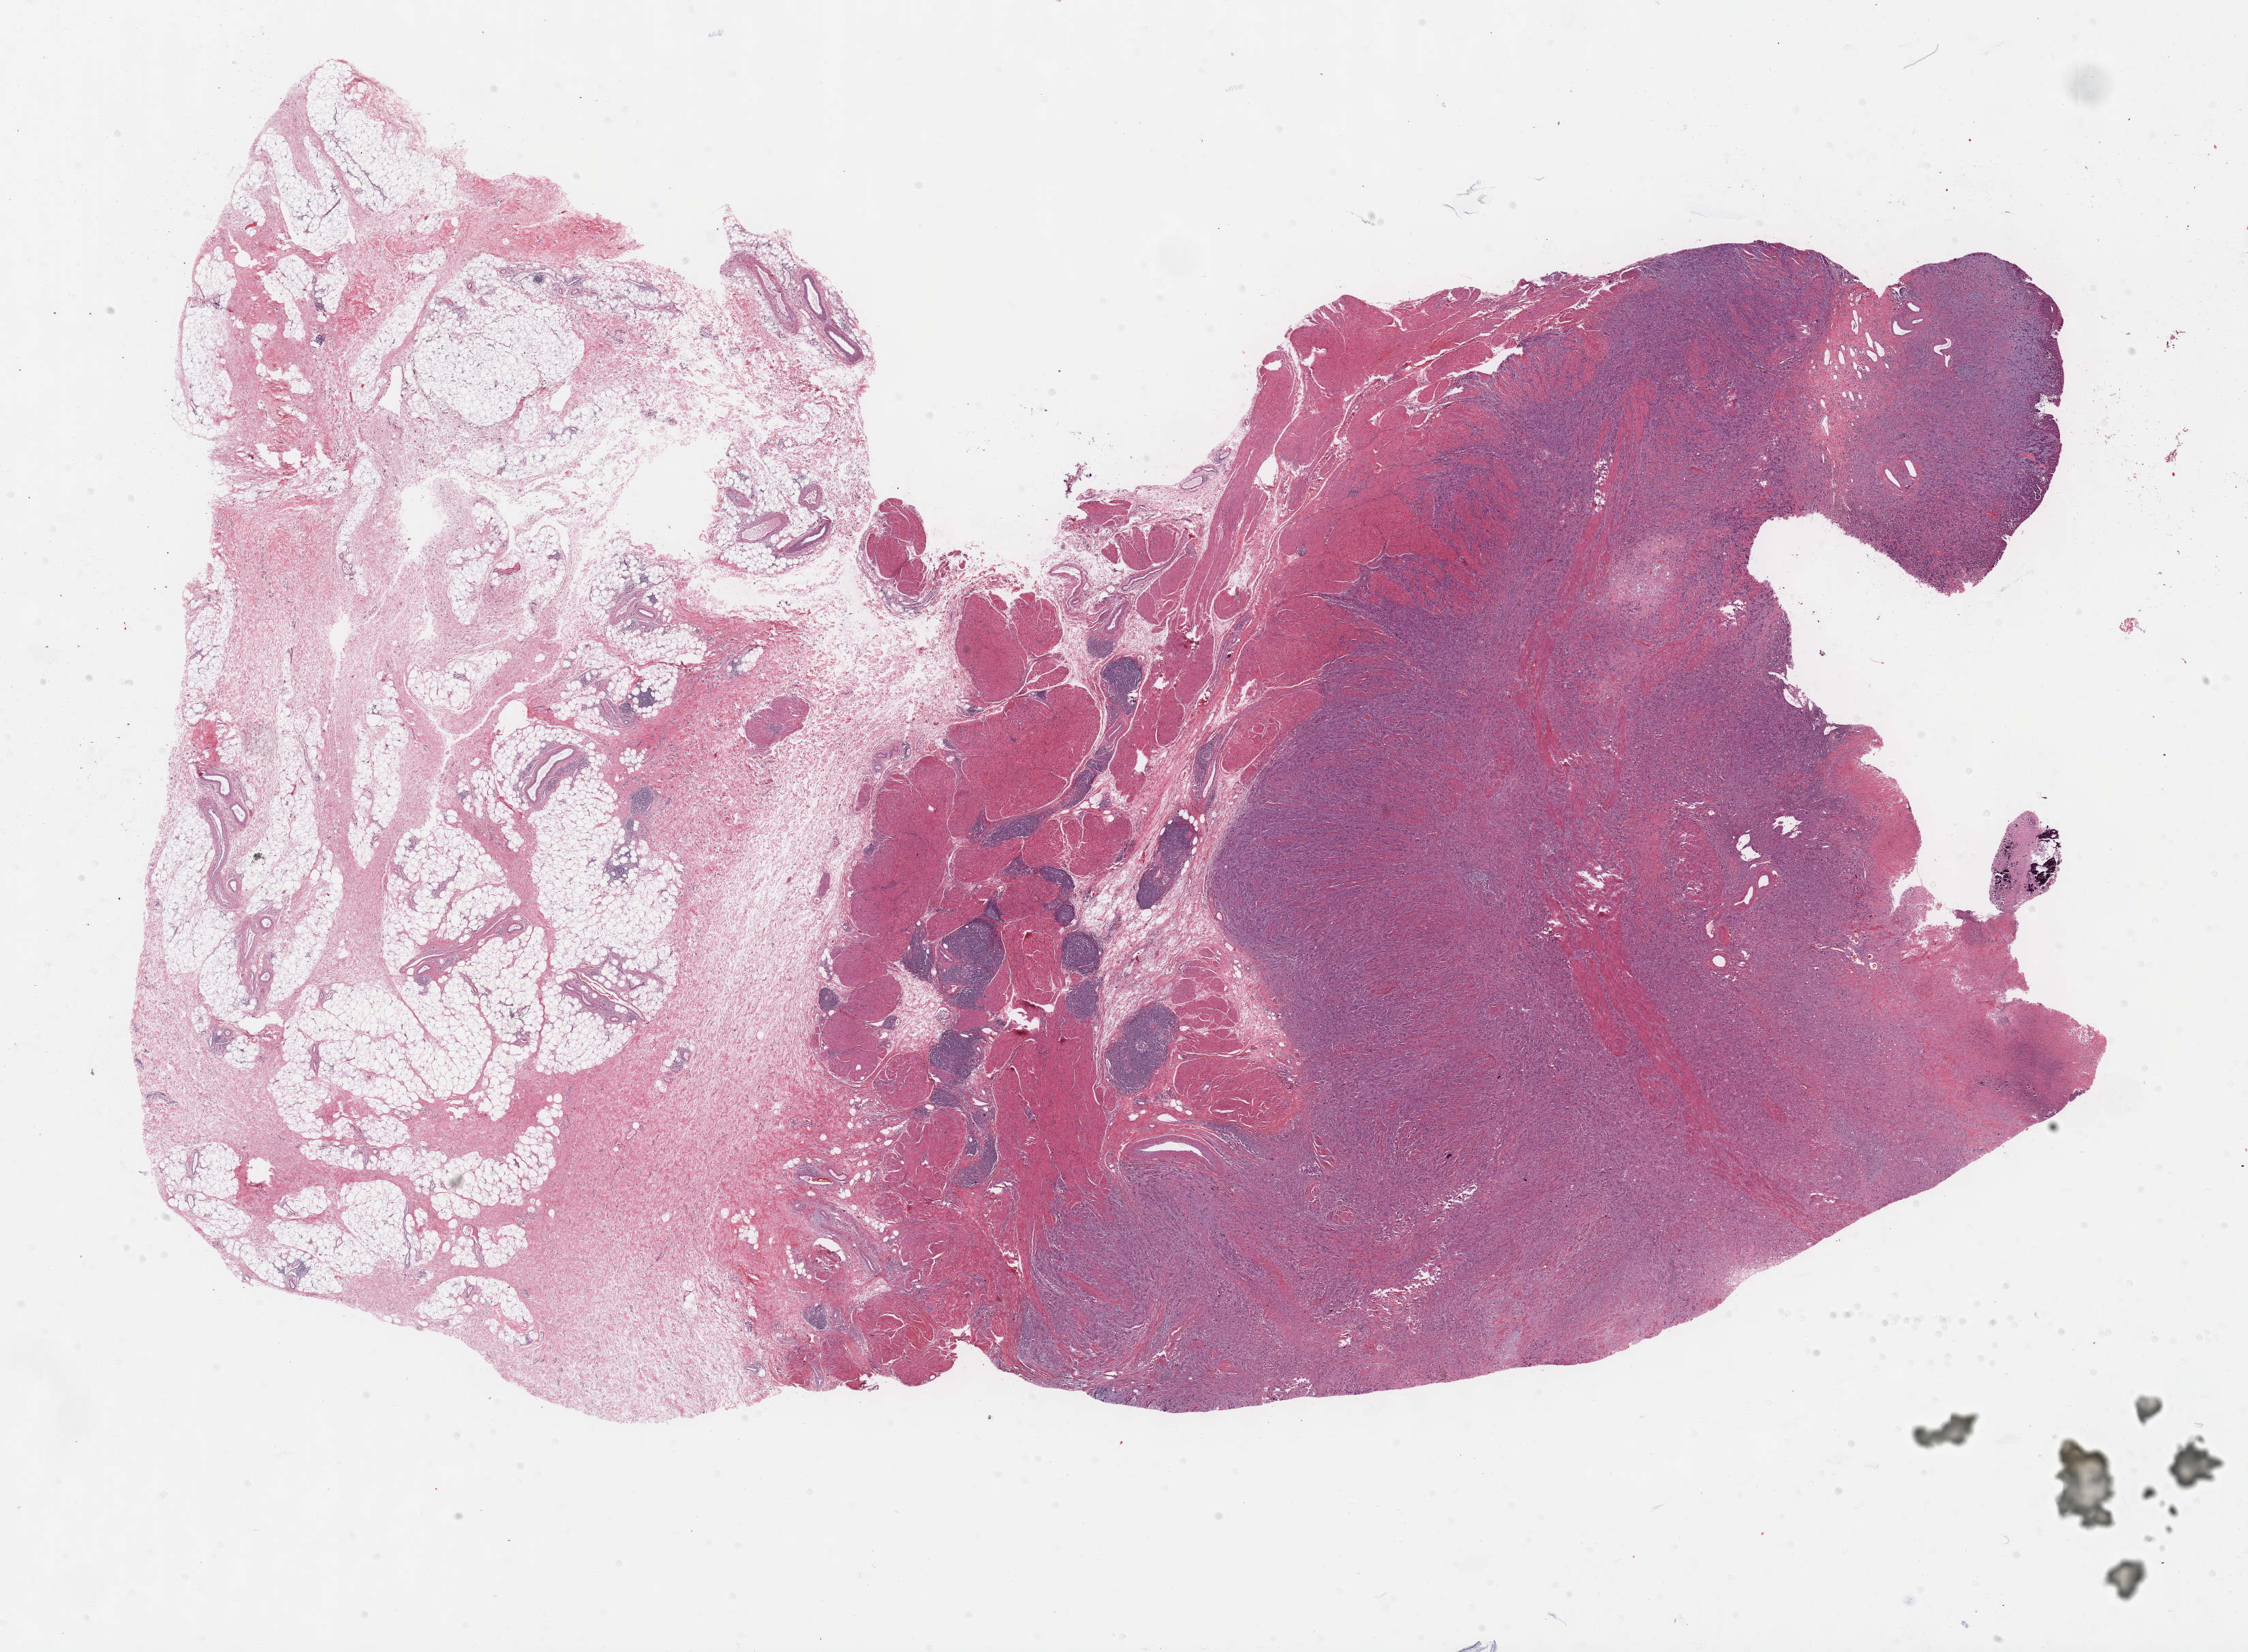
Whole-slide histology image, H&E — whole scanned area (about 26.7 x 19.6 mm, slide scanned at 40x) shown as a low-resolution overview. FFPE section. Sample: primary tumour, bladder. Patient: female, age at initial diagnosis 63 years. Histologic grade: high grade.
- pathologic diagnosis: Transitional cell carcinoma
- AJCC pathologic stage: IV
- TNM: T3b N2 MX
- lymph nodes positive (case pathology): 6 of 71 examined